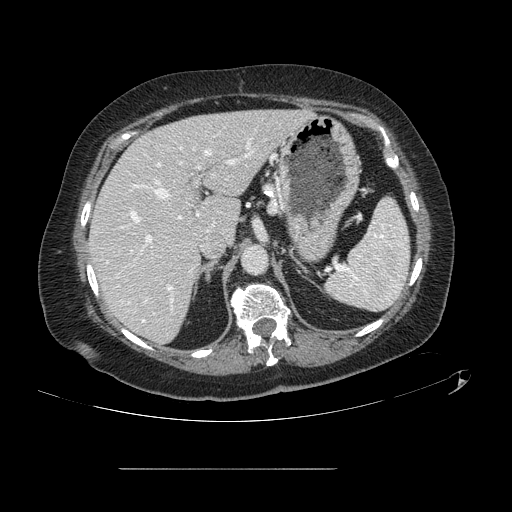
Contrast-enhanced abdominal CT, one axial slice; position 86 of 148 along the scan axis; intravenous contrast given; soft-tissue window (W 400 / L 40 HU); 2.5 mm slice thickness; 512 × 512 image matrix. Female patient, age 75 years. From the clinical record (not read from this slice): diagnosis: colorectal cancer liver metastases, imaged before liver resection; multiple liver metastases: no; largest metastasis: 2.4 cm; disease in both lobes: no.
Outlined on this slice (outlined manually by an expert reader):
- hepatic veins: bounding box (x1, y1, x2, y2) in pixels: (142, 151, 210, 322)
- liver: (90, 110, 308, 343)
- planned liver remnant (the part of the liver to remain after resection): (90, 110, 309, 343)
- portal vein (with intrahepatic branches): (131, 138, 254, 290)